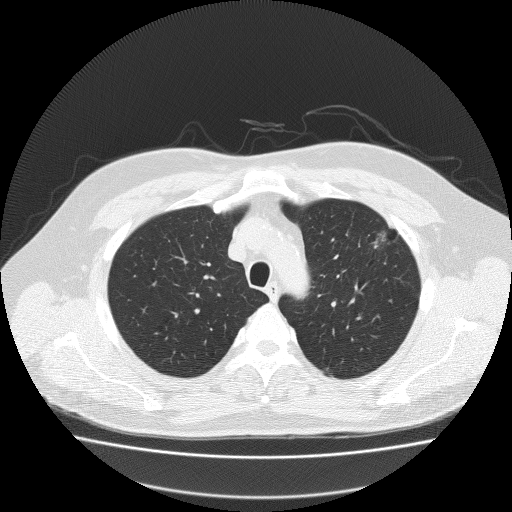
Low-dose screening chest CT, one axial slice. Slice 160 of 204 in the series (ordered by position). Reconstruction kernel FC51. Lung window (W 1500 / L -600 HU). 512 × 512 image matrix, field of view 410 × 410 mm.
Annotated regions visible in this slice (manually delineated by an expert):
- lesion 1 (tumor, upper lobe of left lung): bounding box <375,227,390,248> (left, top, right, bottom; pixels)